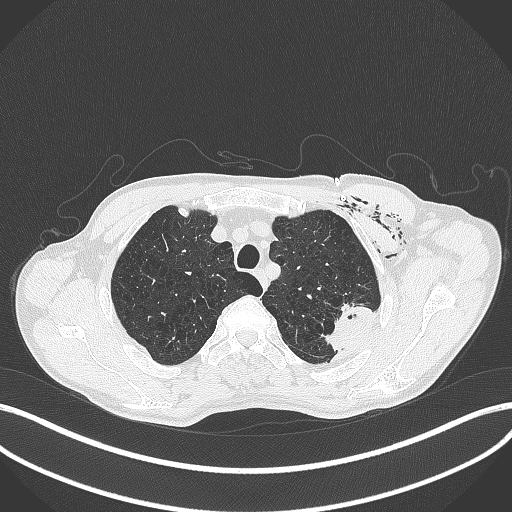
Chest CT, one axial slice. Slice 343 of 457 in the series (ordered by position). Reconstruction kernel B70f. 120 kVp. Lung window (W 1500 / L -600 HU). 1 mm slice thickness. 512 × 512 image matrix, field of view 400 × 400 mm. Patient: male, 58 years. From the clinical record (not read from this slice): clinical TNM (as recorded): T3 N0 M0.
Annotated regions visible in this slice (bounding box drawn by a radiologist):
- lung tumour (recorded histology: adenocarcinoma): bounding box [x1, y1, x2, y2] px = [317, 302, 378, 352]